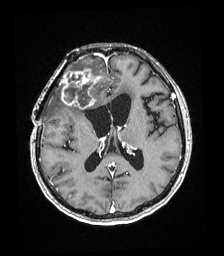
Brain MRI from a brain-tumour surgery series, one axial slice. Position 90 of 192 along the scan axis. T1-weighted post-contrast. 224 × 256 image matrix, field of view 219 × 250 mm. From the clinical record (not read from this slice): histopathology: Astrocytoma; WHO grade: 4; IDH mutation: yes.
Outlined on this slice (expert manual segmentation):
- tumour: bounding box [x1, y1, x2, y2] px = [61, 69, 103, 108]